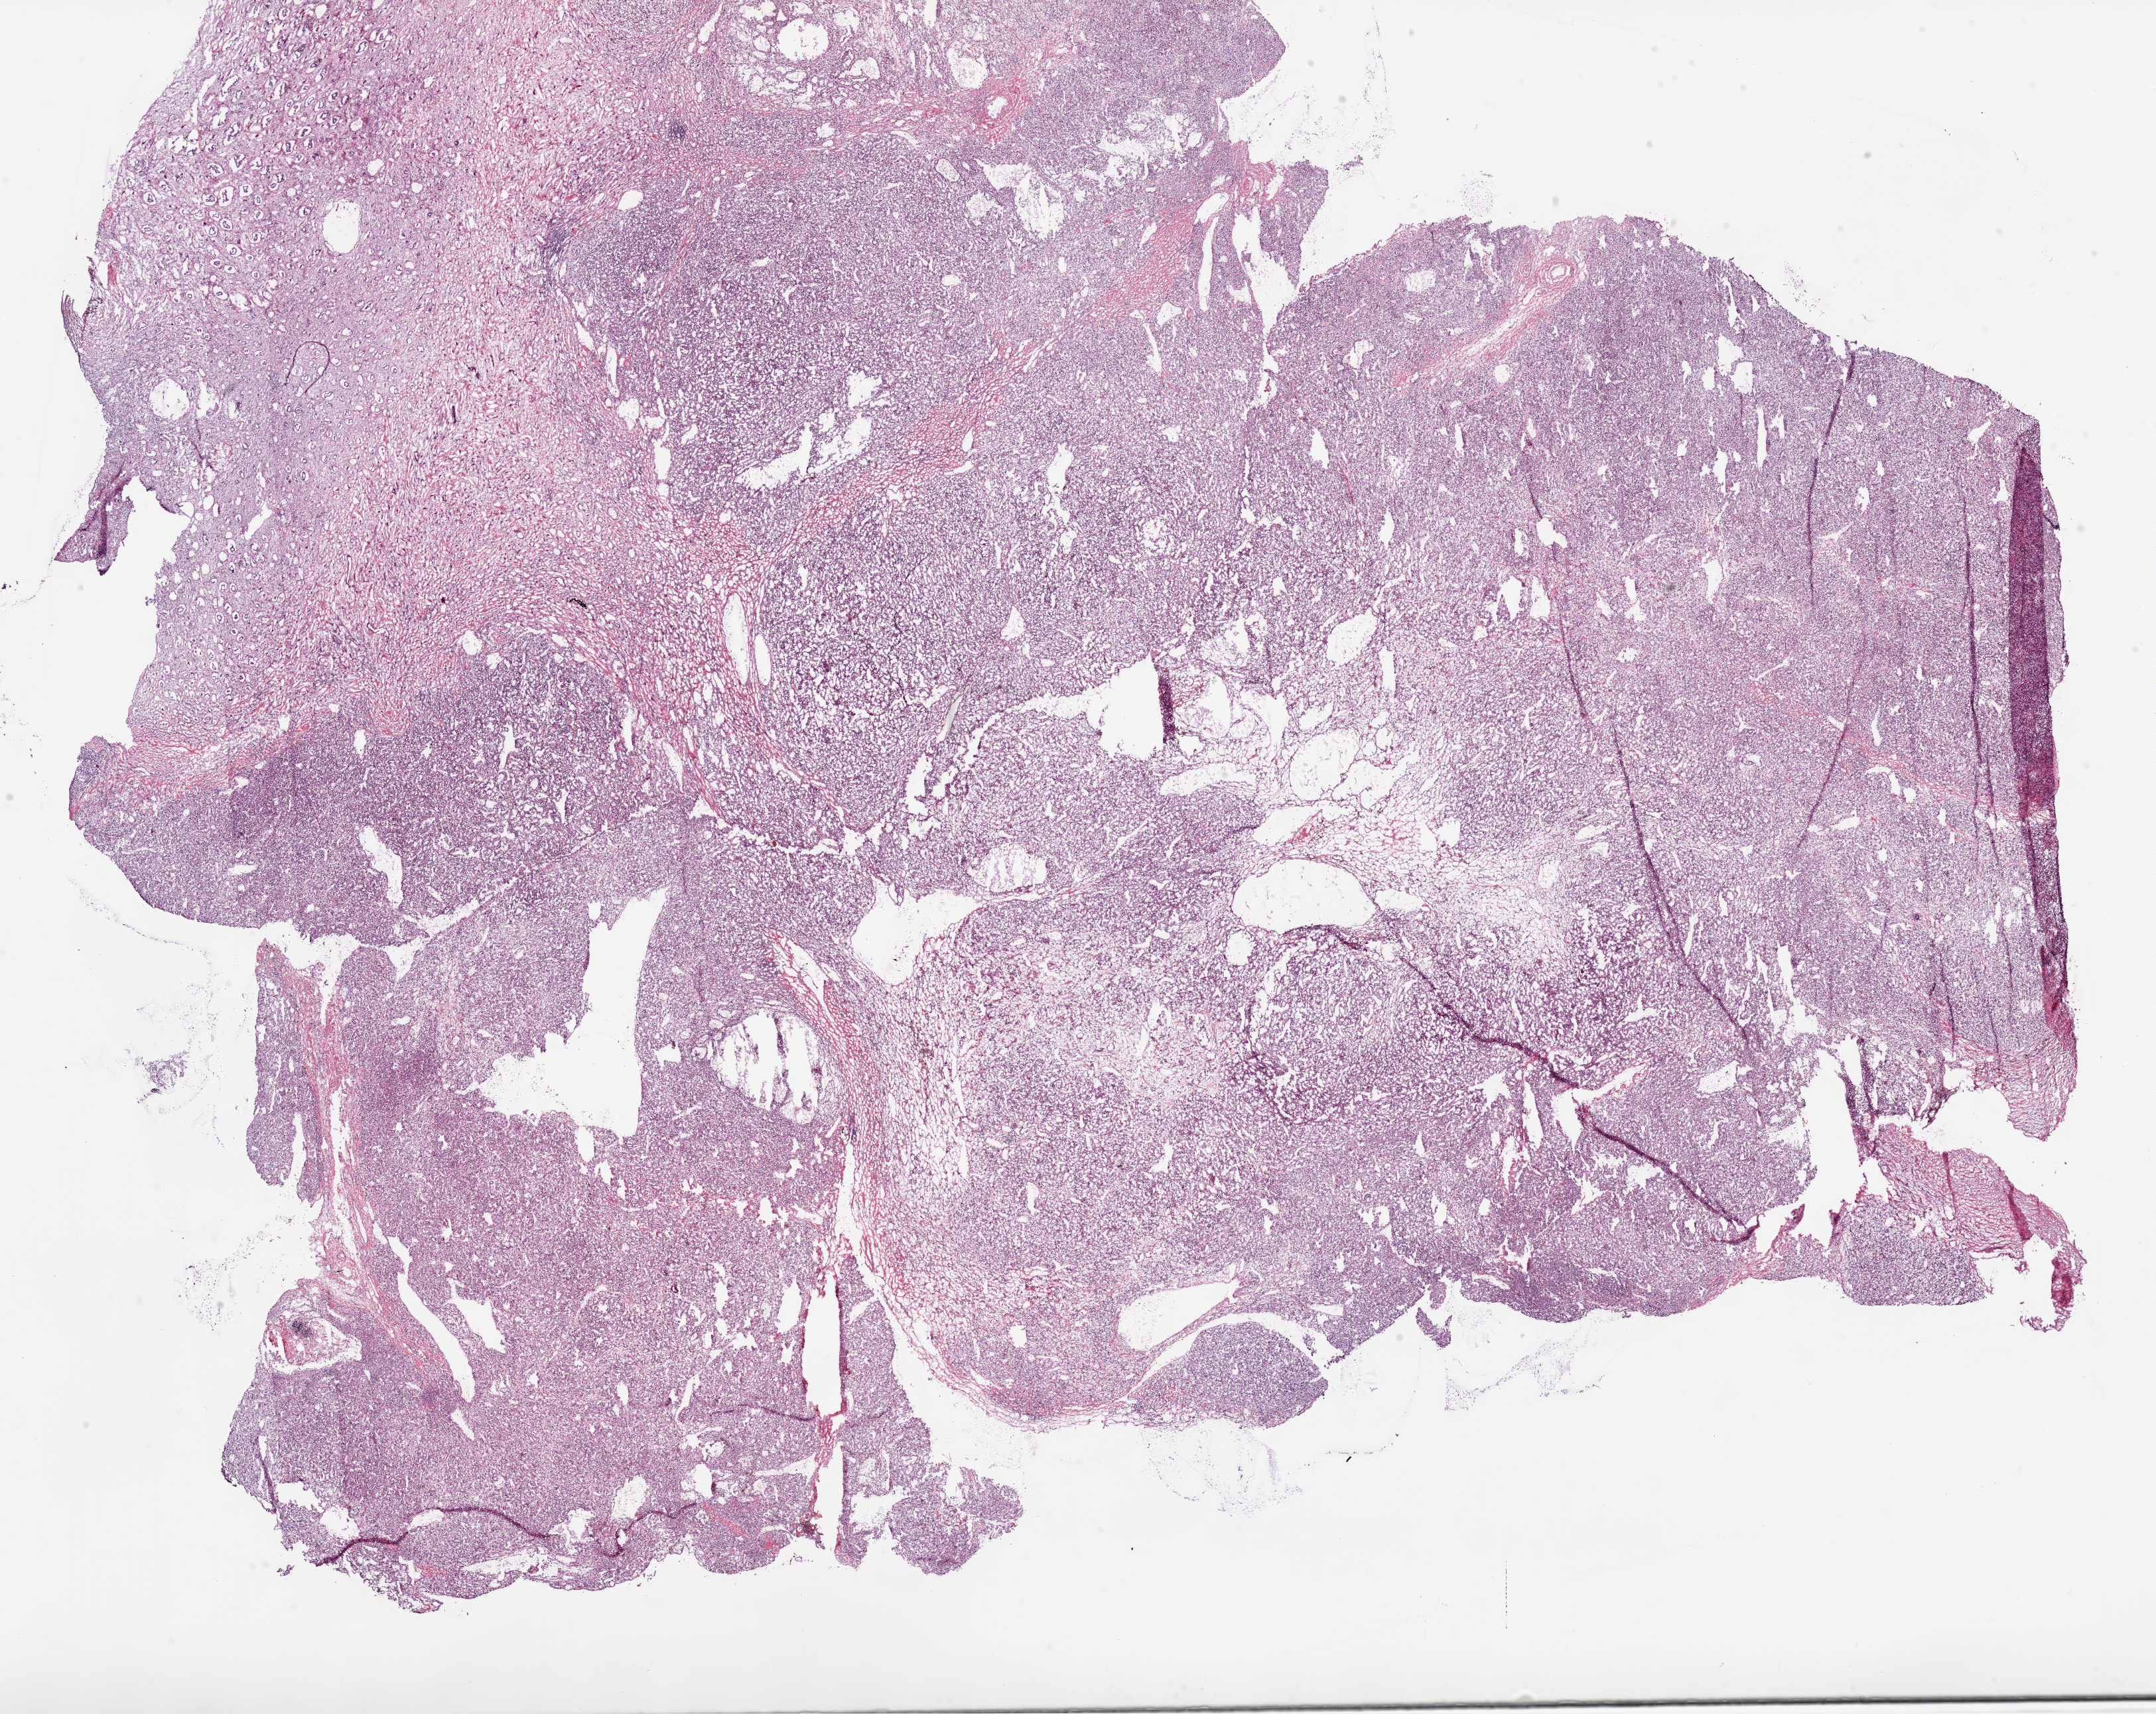
Whole-slide histology image, H&E — whole scanned area (about 26.1 x 20.7 mm) shown as a low-resolution overview, frozen section, kidney, primary tumour sample. Male patient; age at initial diagnosis 48 years. Histologic grade: G3 (poorly differentiated). Composition of this section per pathologist review: tumour cells 70%, tumour nuclei 75%, normal cells 20%, stromal cells 10%, necrosis 0%.
• AJCC pathologic stage: III
• diagnosis: Clear cell adenocarcinoma, NOS
• lymph nodes positive (case pathology): 0 of 3 examined